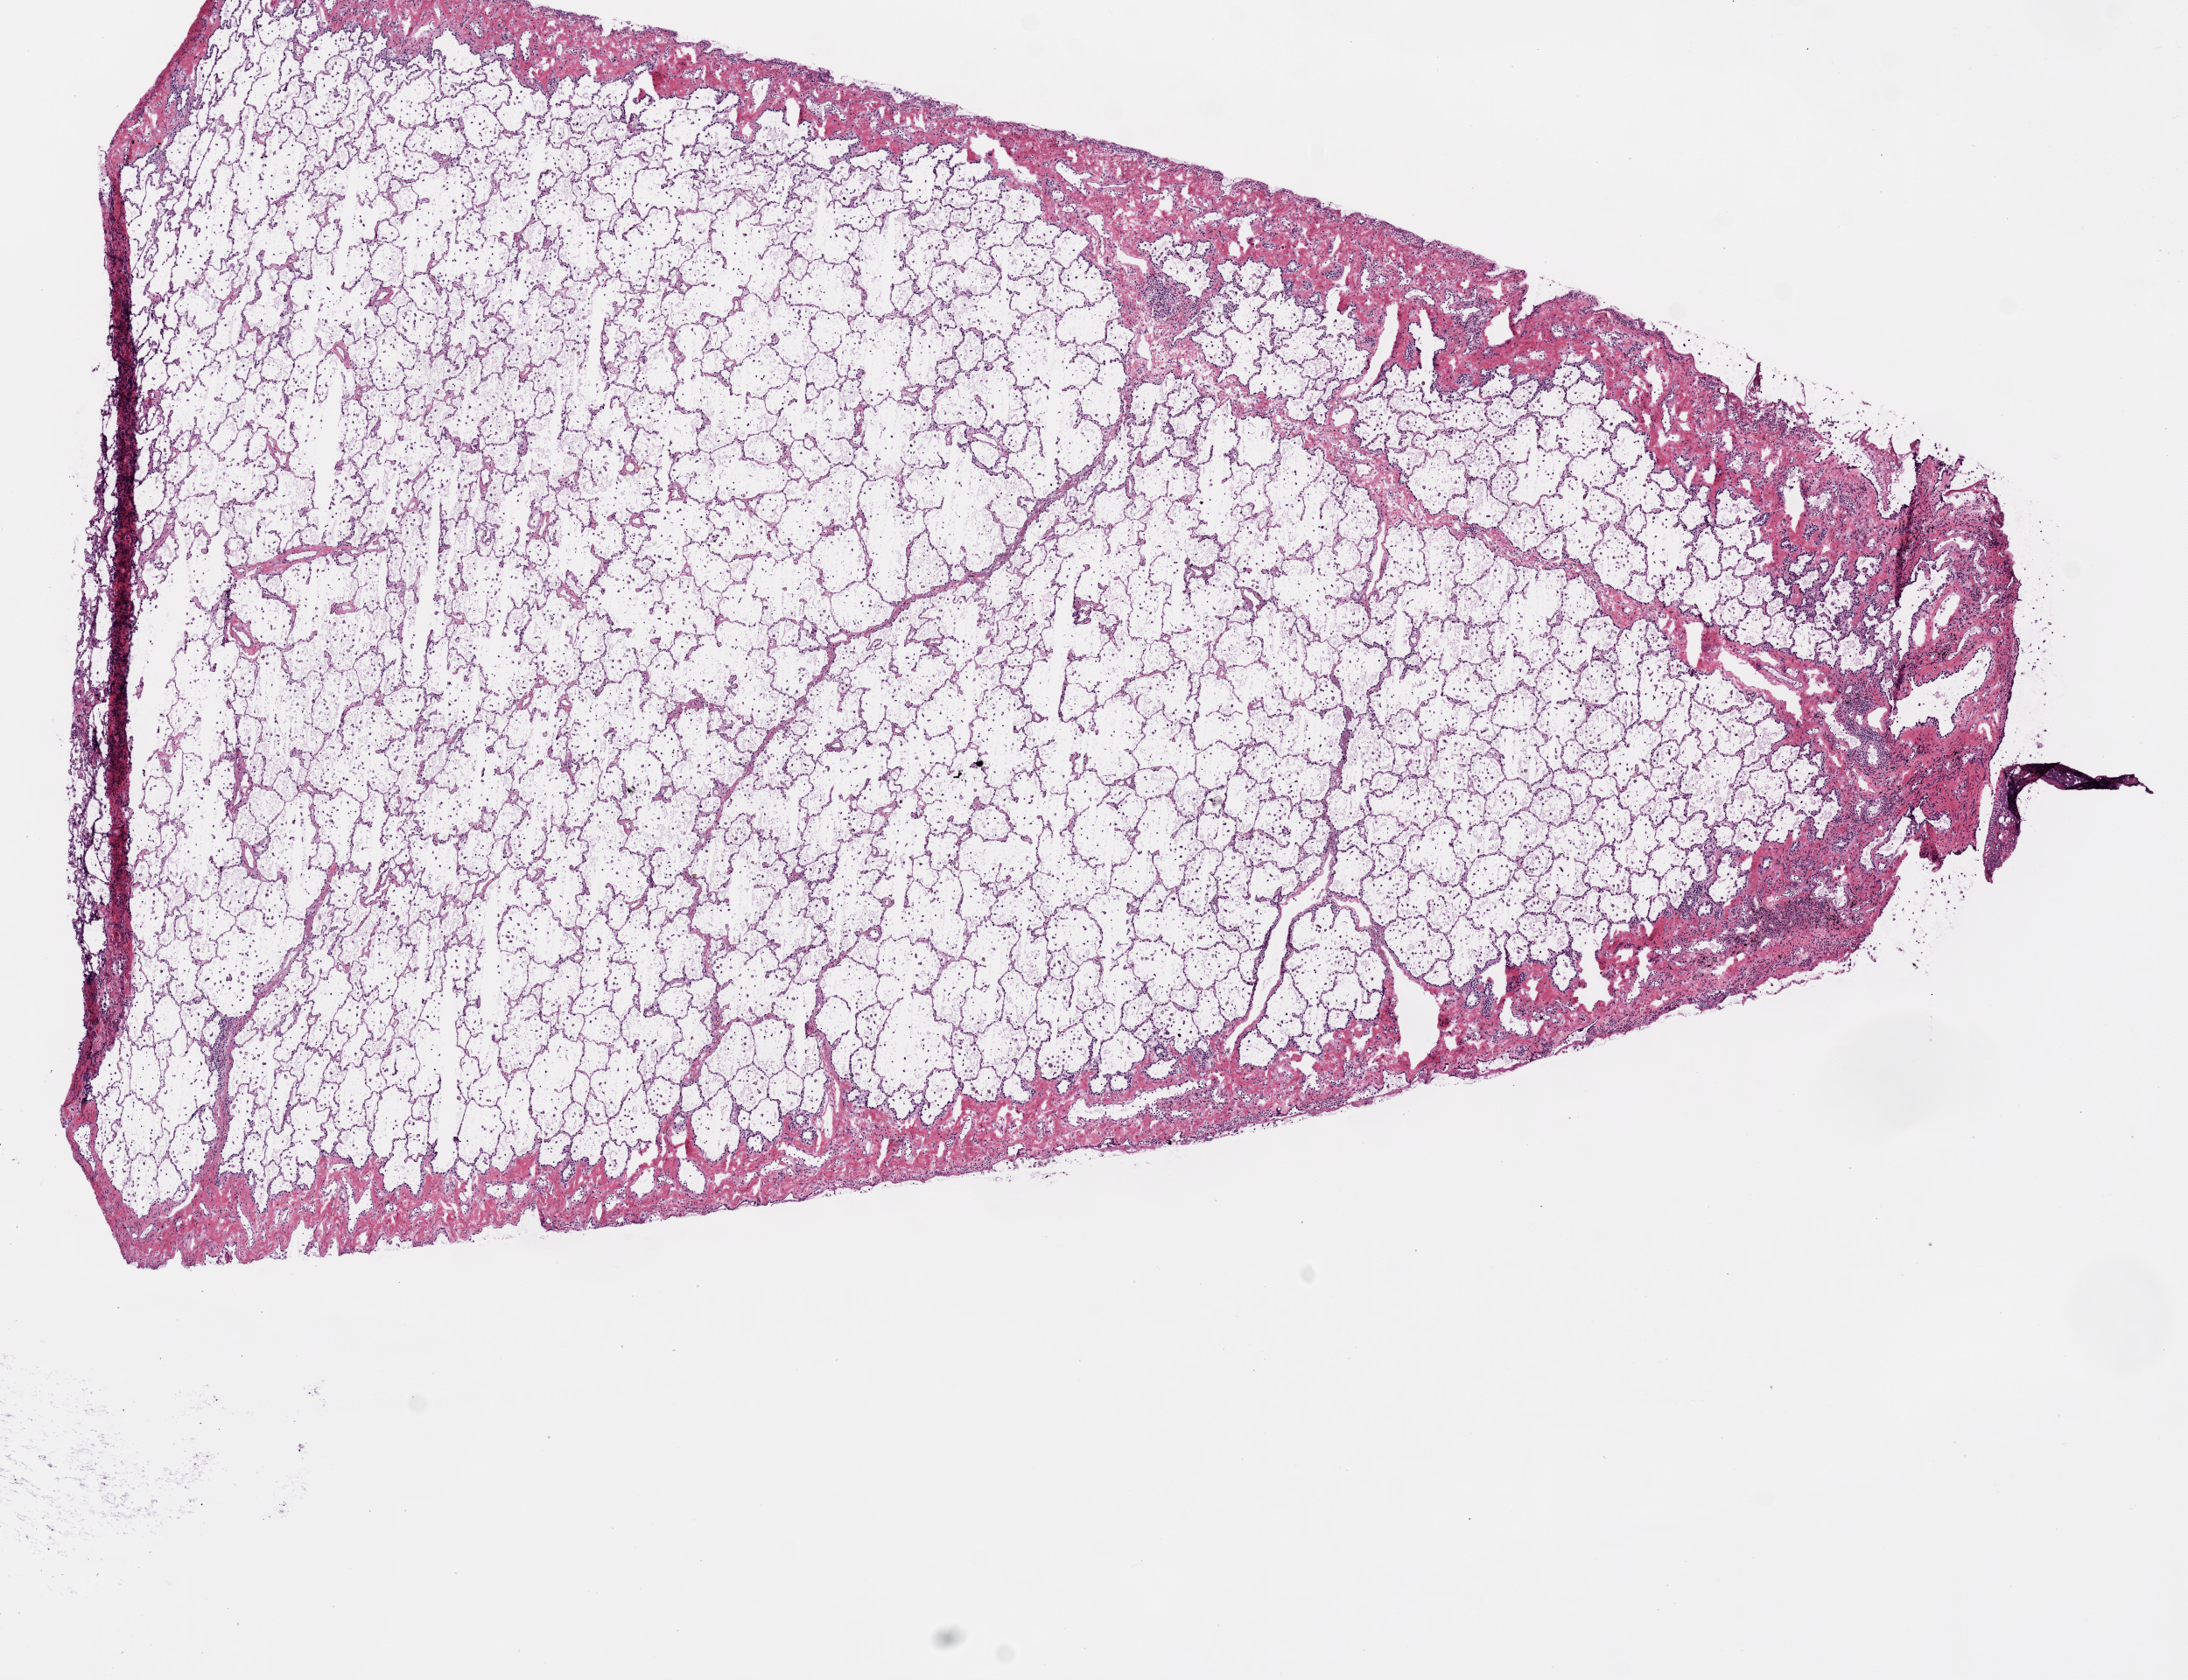
Whole-slide histology image, H&E-stained — whole scanned area (about 10.0 x 7.7 mm) shown as a low-resolution overview; frozen section from the top of the tissue portion; solid tissue normal (non-tumour tissue) sample from the lung. Male patient; age at initial diagnosis 42 years.
* this section: solid tissue normal (non-tumour) sample from the same patient
* patient diagnosis: Adenocarcinoma, NOS